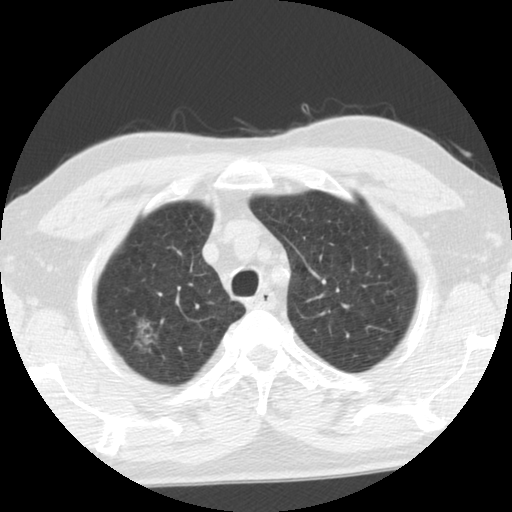
Low-dose screening chest CT, axial slice; second annual screen; lung window (W 1500 / L -600 HU); 2.5 mm slice thickness; slice 94 of 116 in the series. Male participant, aged 68 years at enrolment. Former smoker at enrolment.
Expert reader's lesion annotation, bounding box <128,315,162,353> (left, top, right, bottom; pixels). Reader record for this screening exam (exam-level; its link to the box is not recorded): non-calcified nodule or mass ≥4 mm, right upper lobe, poorly defined margins, ground glass attenuation, pre-existing on the prior screen: yes; interval growth: yes. Official screen result: positive, other. Later outcome: lung cancer diagnosed 88 days after this screen — adenocarcinoma, NOS, right upper lobe, moderately differentiated (G2), stage IA (AJCC 6th edition), 28 mm at pathology.